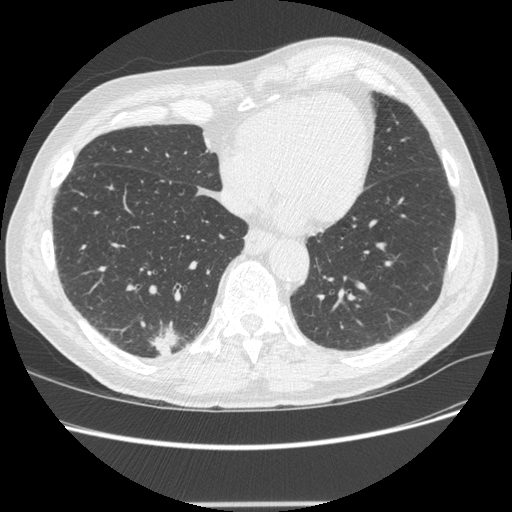
Low-dose screening chest CT, one axial slice. Position 74 of 245 along the scan axis. Reconstruction kernel STANDARD. Lung window (W 1500 / L -600 HU). 1.25 mm slice thickness. 512 × 512 image matrix, field of view 372 × 372 mm.
Structures marked on this image (expert manual segmentation):
- lesion 1 (tumor, lower lobe of right lung): box from (x=150, y=325) to (x=180, y=356) px